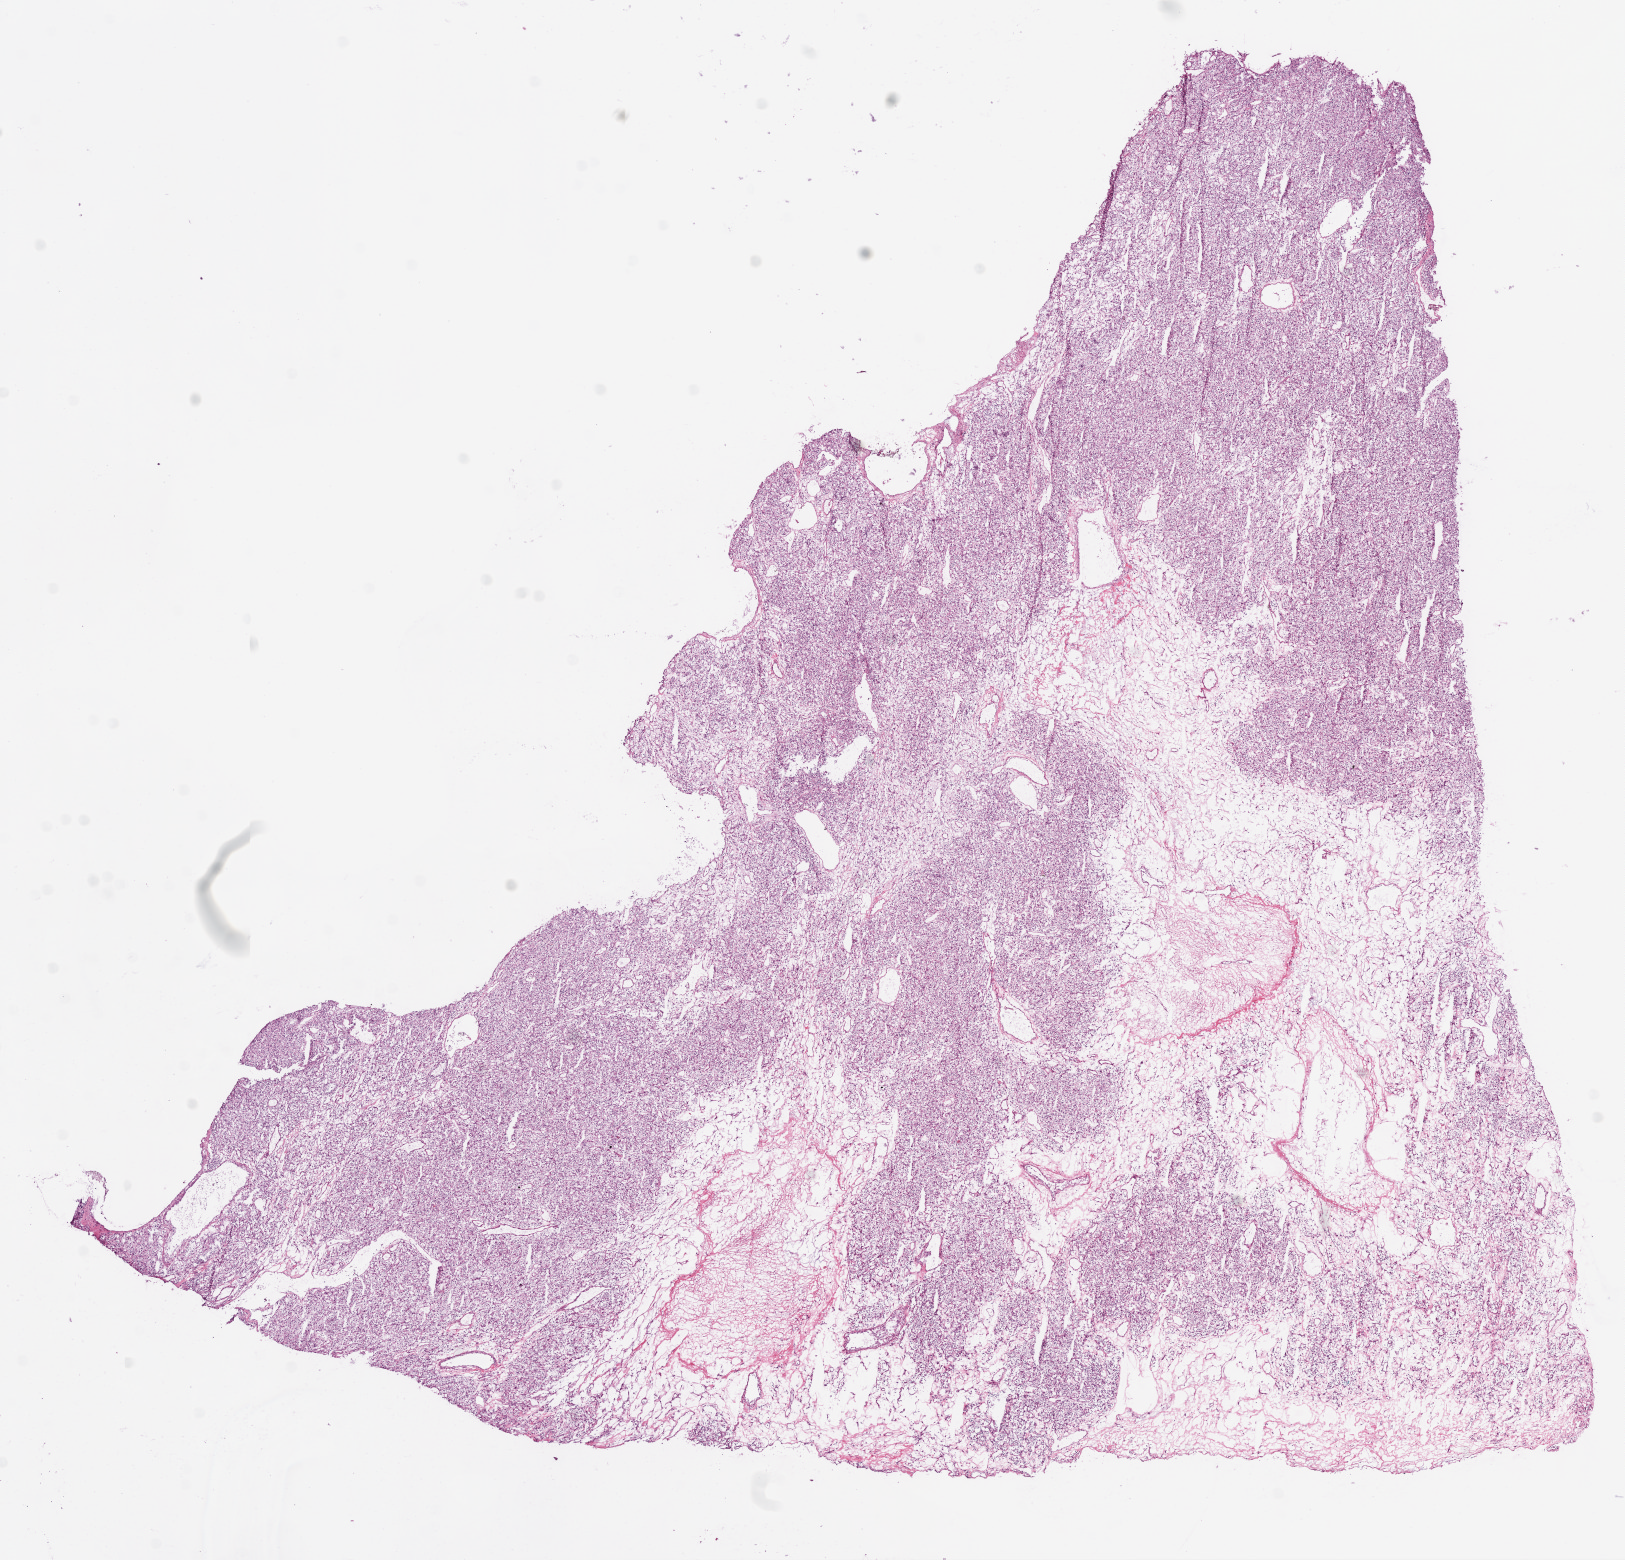
Whole-slide histology image, H&E, whole scanned area (about 13.0 x 12.5 mm) shown as a low-resolution overview, frozen section, primary tumour sample from the kidney. Male patient; age at initial diagnosis 70 years. Histologic grade: G2 (moderately differentiated). Slide review estimates, as recorded: tumour cells 65%, tumour nuclei 85%, normal cells 0%, stromal cells 35%, necrosis 0%.
Diagnosis: Clear cell adenocarcinoma, NOS. TNM: T1b N0 M0. AJCC pathologic stage: I. Laterality: right.